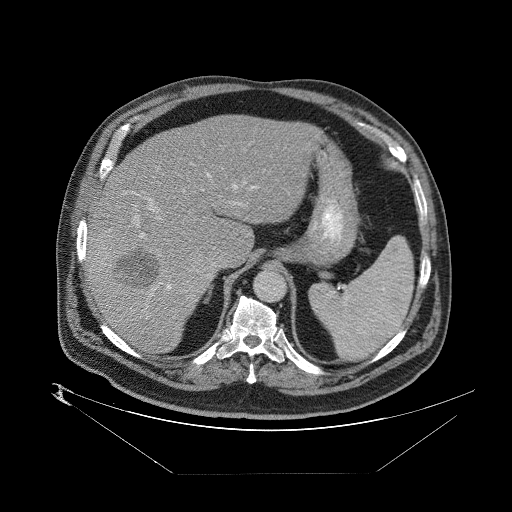
Contrast-enhanced abdominal CT (liver protocol), one axial slice; slice 57 of 89 in the series (ordered by position); reconstruction kernel STANDARD; 140 kVp; one of 2 acquisitions stored at this slice position; soft-tissue window (W 400 / L 40 HU); 2.5 mm slice thickness; 512 × 512 image matrix, field of view 480 × 480 mm. Case-level facts recorded for this patient, not image findings: diagnosis: hepatocellular carcinoma (patient treated with transarterial chemoembolisation; whether this scan precedes or follows treatment is not stated here); TNM stage (as recorded): Stage-II; Child-Pugh class: B; tumour differentiation: moderately differentiated; tumour size: 4 cm.
Annotated regions visible in this slice (semi-automatically segmented with operator editing):
- abdominal aorta: bounding box (x1, y1, x2, y2) in pixels: (254, 268, 286, 301)
- liver parenchyma outside the tumour (the mass and vessels are separate outlines, so this box may not span the whole liver): (87, 112, 313, 352)
- mass: (91, 239, 228, 299)
- liver vessels: (89, 154, 271, 306)